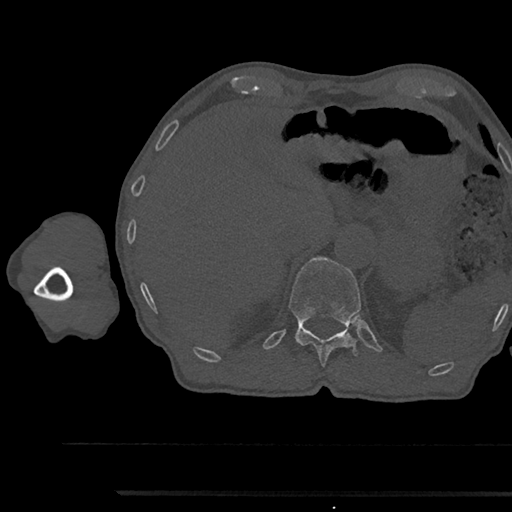
CT including the spine, one axial slice; slice 711 of 797 in the series (ordered by position); 120 kVp; bone window (W 1800 / L 400 HU); 0.5 mm slice thickness; 512 × 512 image matrix, field of view 367 × 367 mm. Patient: male, 79 years. Case-level facts recorded for this patient, not image findings: primary cancer: prostate.
Annotated regions visible in this slice (semi-automatic segmentation, software-assisted and operator-edited):
- T12 vertebra: bounding box <289,257,361,367> (left, top, right, bottom; pixels)